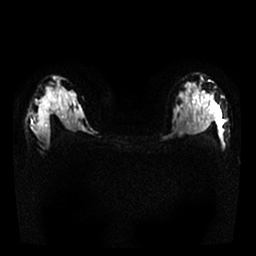
Breast MRI, one axial slice; position 15 of 25 along the scan axis; diffusion-weighted series; image 2 of 4 stored at this slice position (different b-values; order by instance number); 1.5 T; 256 × 256 image matrix, field of view 320 × 320 mm. Female patient.
Annotated regions visible in this slice (expert manual segmentation):
- tumour on diffusion-weighted imaging: bounding box (x1, y1, x2, y2) in pixels: (42, 98, 54, 110)